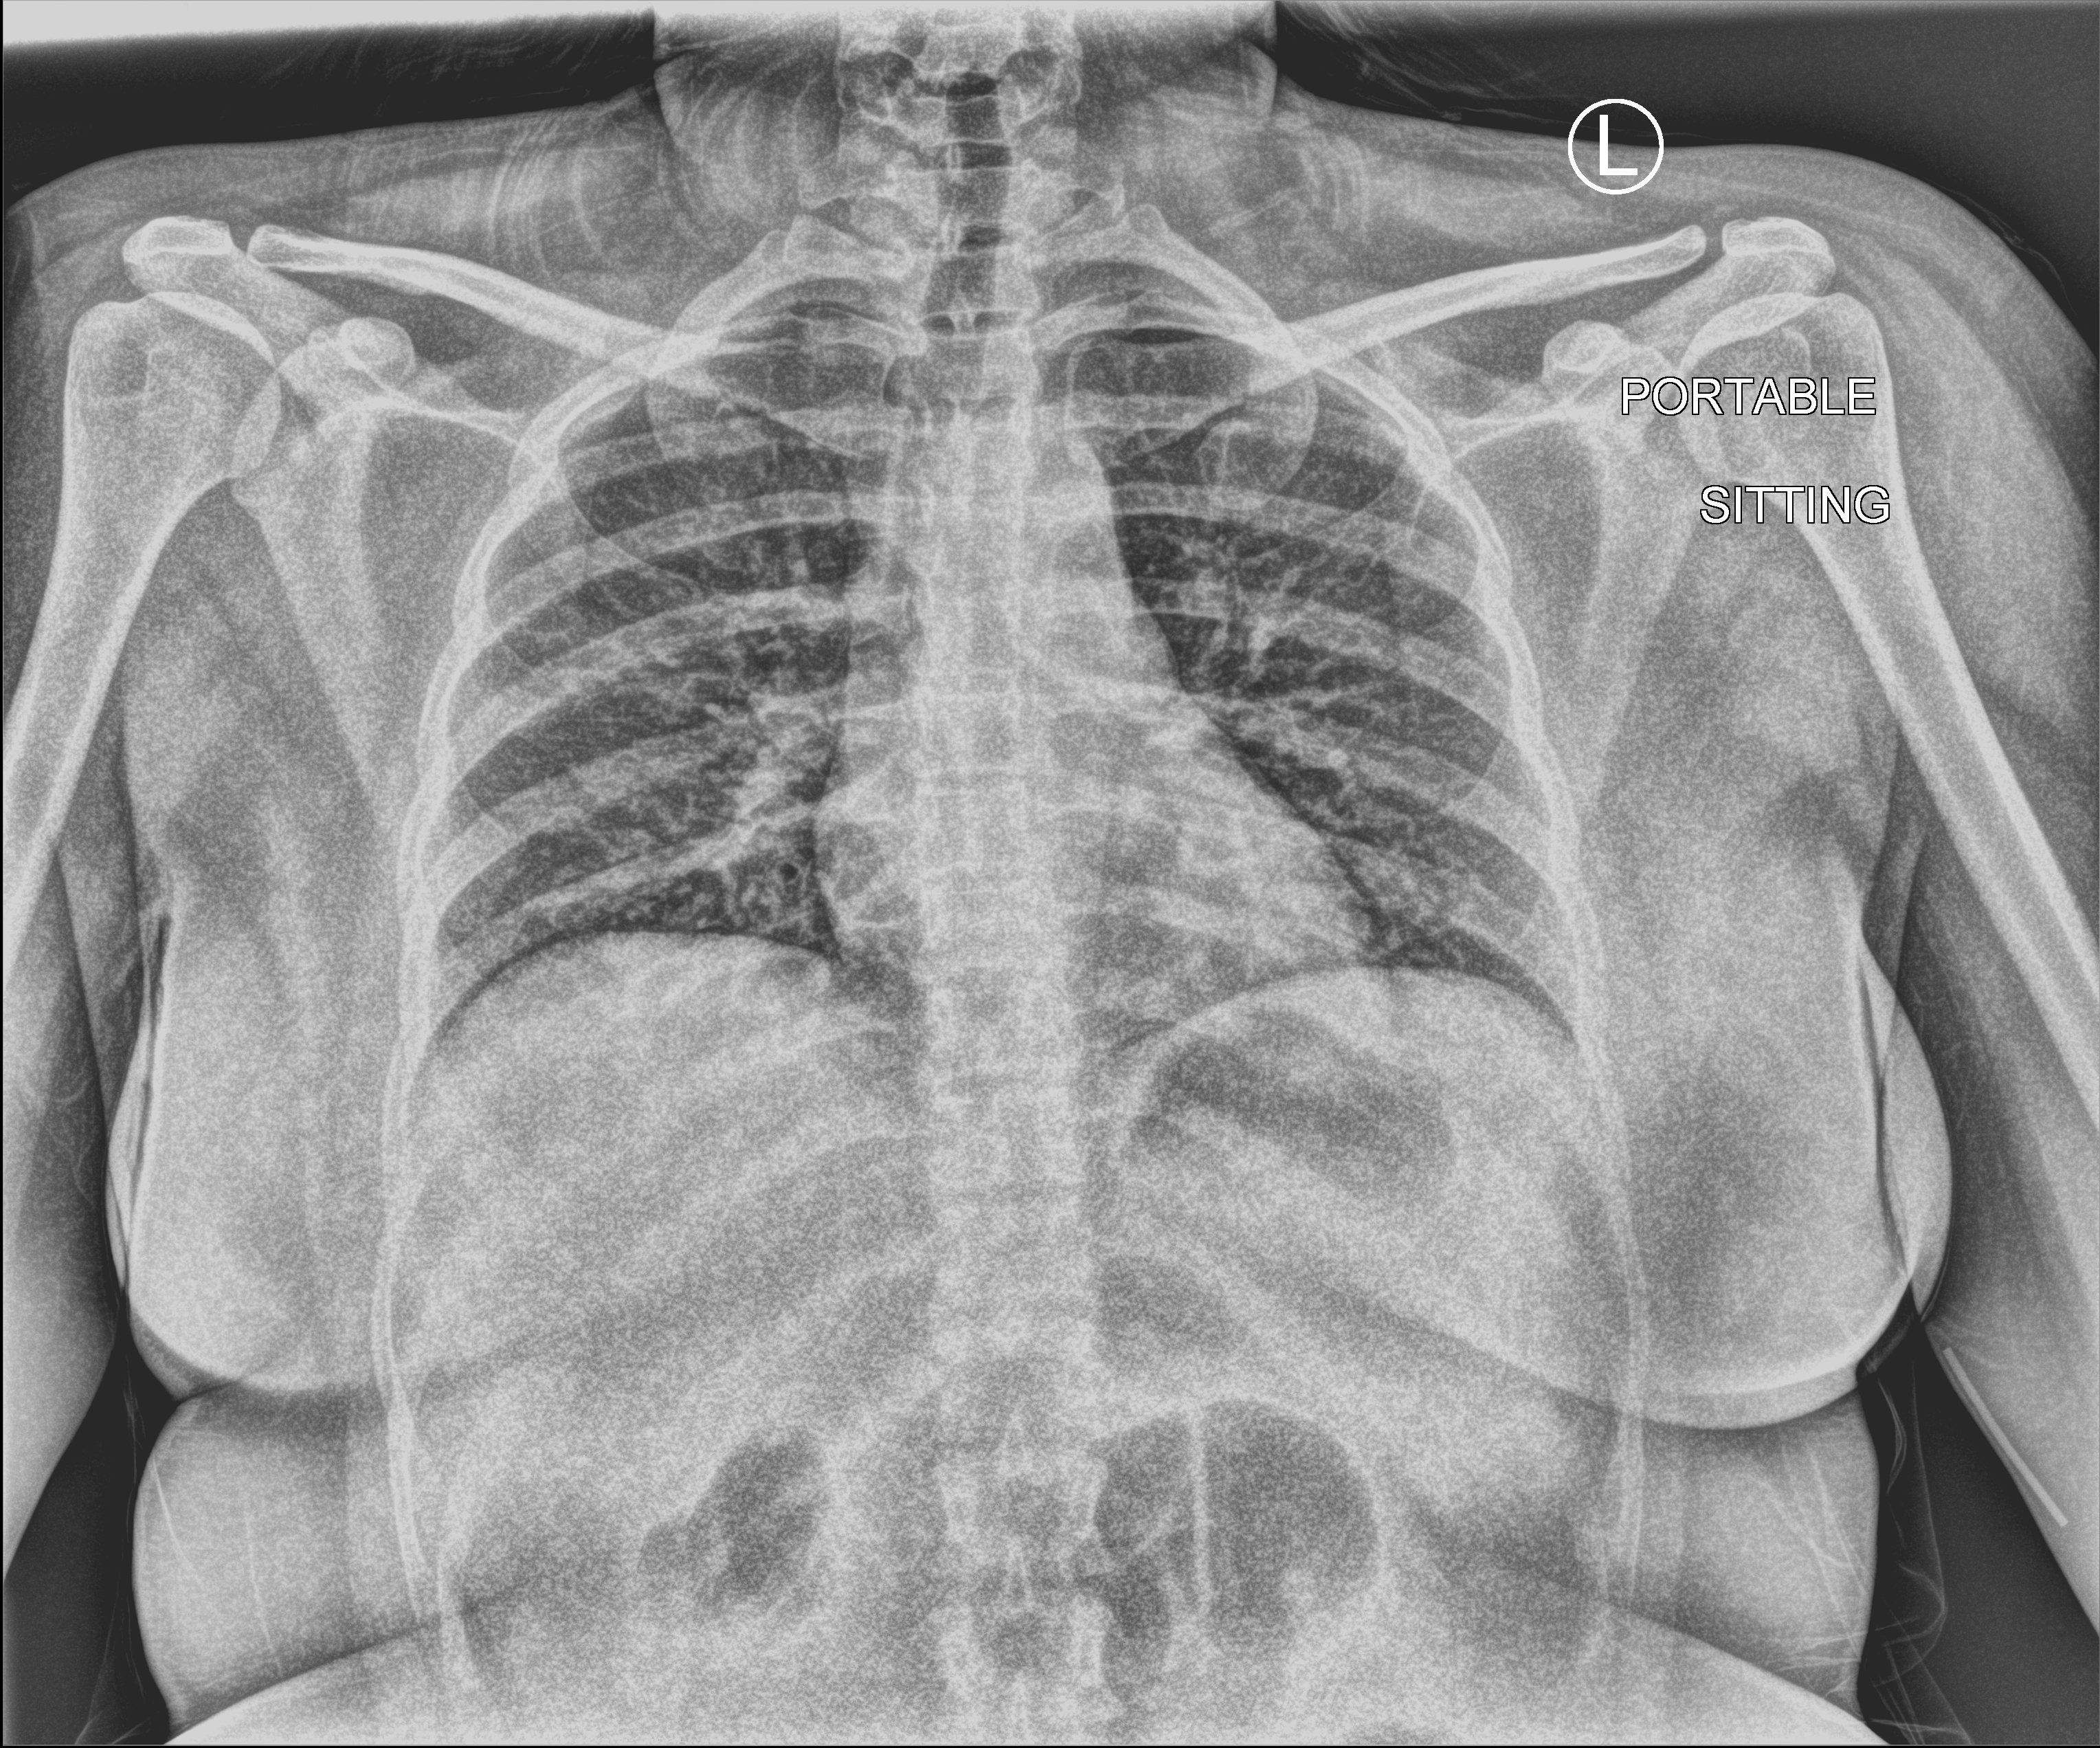
Portable chest radiograph; anteroposterior (AP) projection. Female patient hospitalised with COVID-19, age 18–59 years.
From the hospital-stay record, not from the radiograph (when in the stay this image was taken is not recorded): COPD (admission record): no.